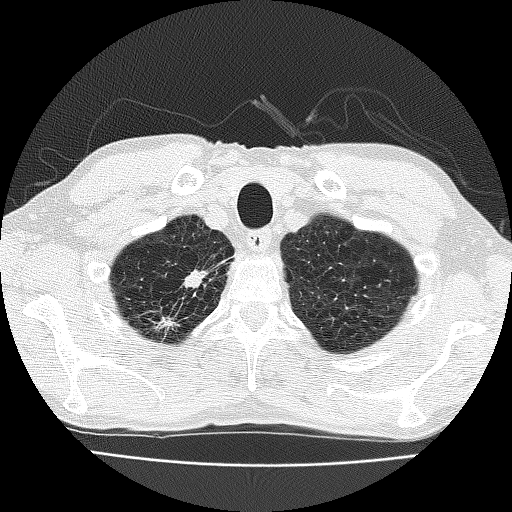
Low-dose screening chest CT, one axial slice; position 157 of 185 along the scan axis; lung window (W 1500 / L -600 HU); 512 × 512 image matrix, field of view 322 × 322 mm.
Structures marked on this image (outlined manually by an expert reader):
- lesion 1 (nodule, upper lobe of right lung): bounding box [x1, y1, x2, y2] px = [184, 270, 206, 288]
- lesion 2 (nodule, upper lobe of right lung): [158, 317, 178, 329]